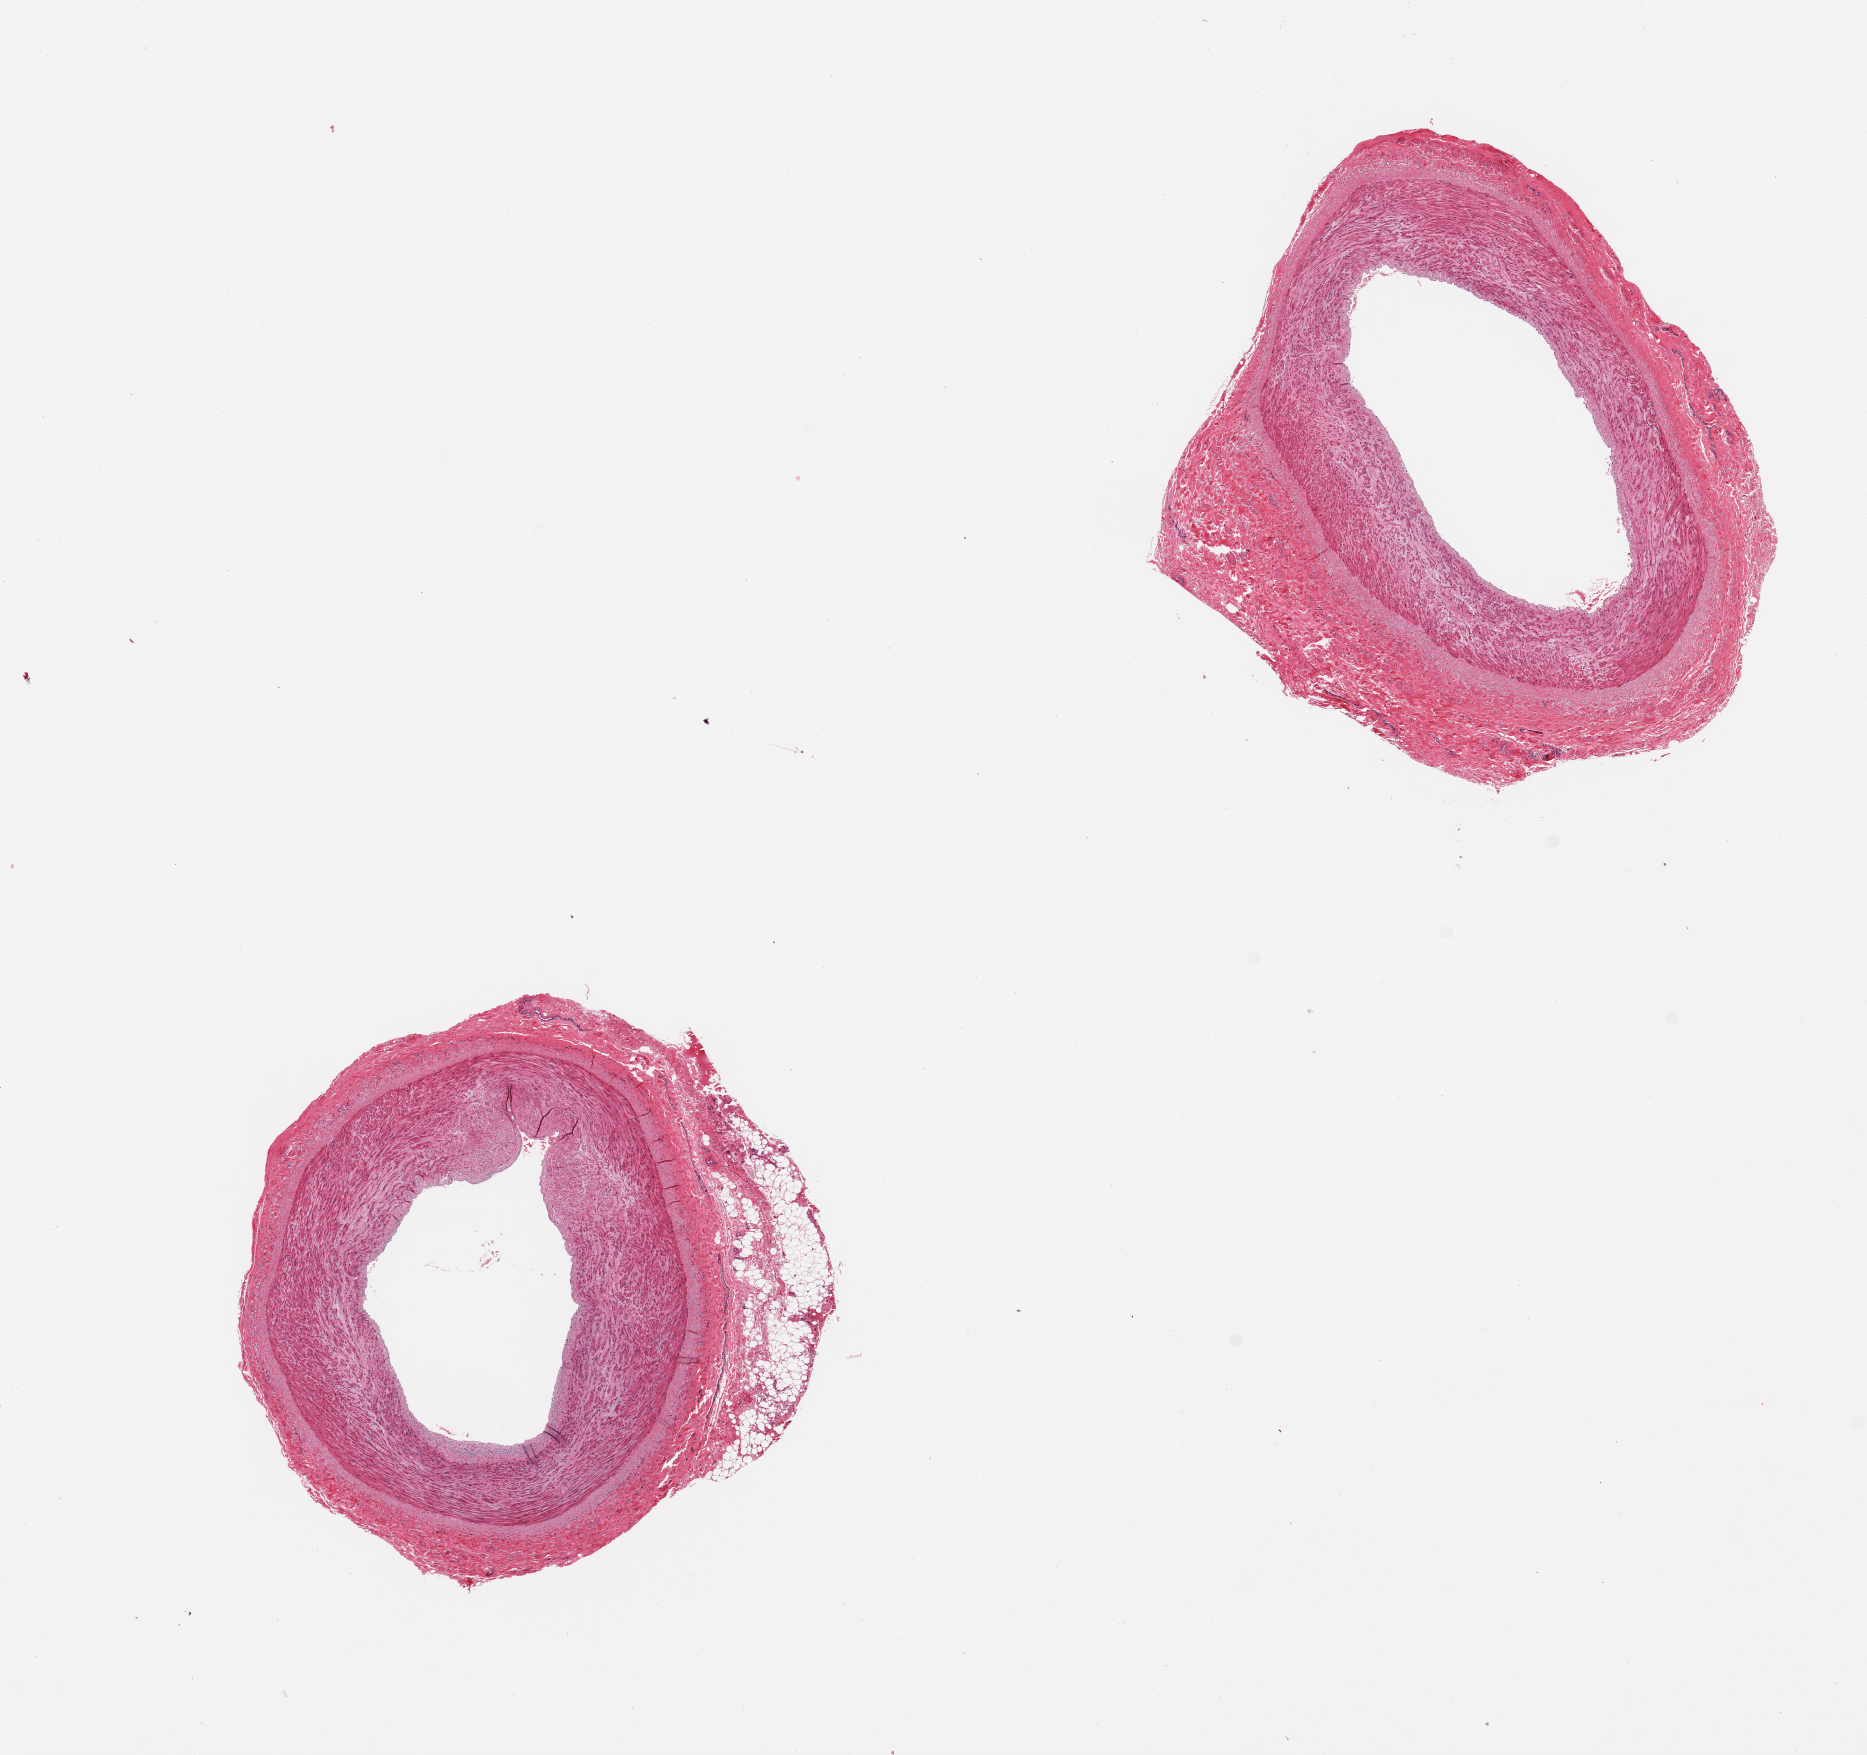
Whole-slide image, H&E stain, a low-resolution overview of the entire scanned area, about 14.8 x 13.9 mm (acquisition: 20x scan). PAXgene-fixed paraffin-embedded (PFPE) section. Section of tibial artery (target tissue). Tissue donor sample.
Pathologist's review note for this sample: 2 pieces. small amount of periadventitial fat and fibrous tissue.